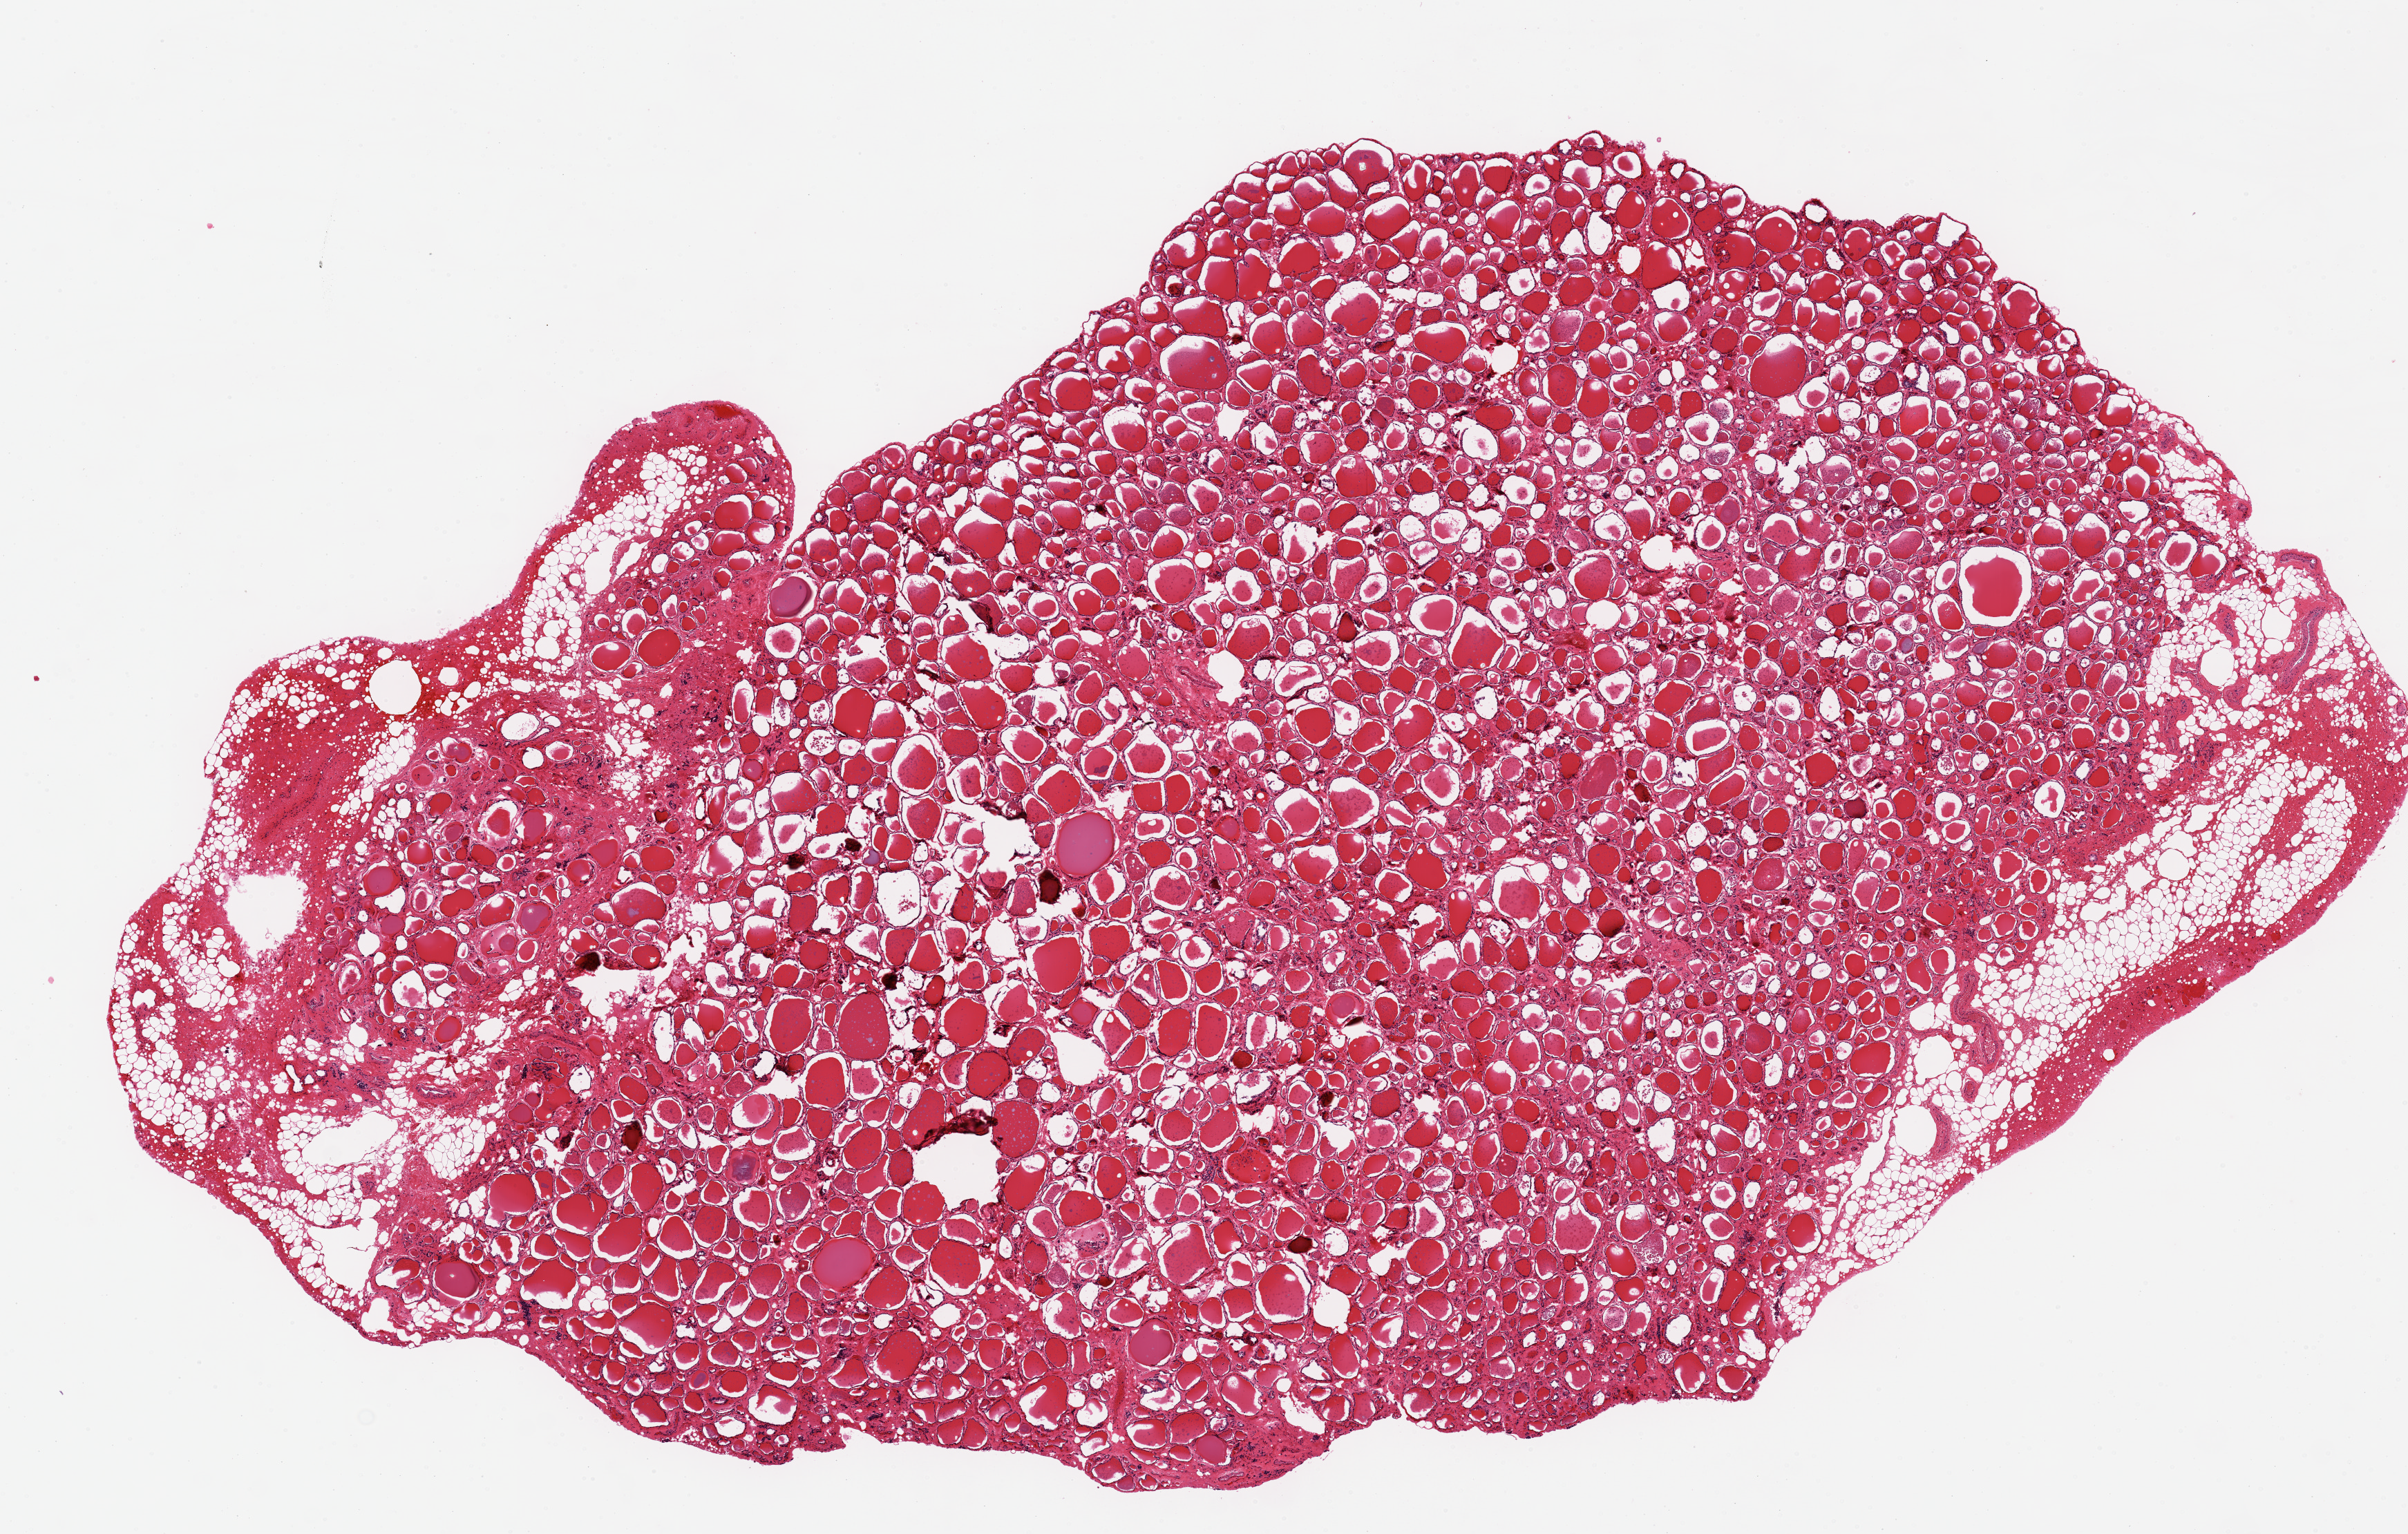
Digitized haematoxylin and eosin-stained section, a low-resolution overview of the entire scanned area, about 13.8 x 8.8 mm (slide scanned at 20x). PAXgene-fixed, paraffin-embedded tissue. Sampled site (target tissue): thyroid. Donor tissue sample. Donor sex: male.
Pathologist's review note for this sample: 1 piece 11x7 mm.